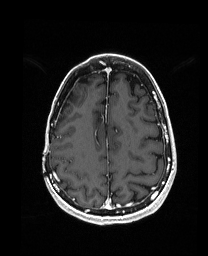
Brain MRI from a brain-tumour surgery series, one axial slice. Slice 54 of 192 in the series (ordered by position). T1-weighted post-contrast. 1 mm slice thickness. 208 × 256 image matrix, field of view 203 × 250 mm. From the clinical record (not read from this slice): histopathology: Metastatic Carcinoma from Breast primary; tumour location: Right Frontal.
Outlined on this slice (manually delineated by an expert):
- previous resection cavity: bounding box <64,92,73,106> (left, top, right, bottom; pixels)